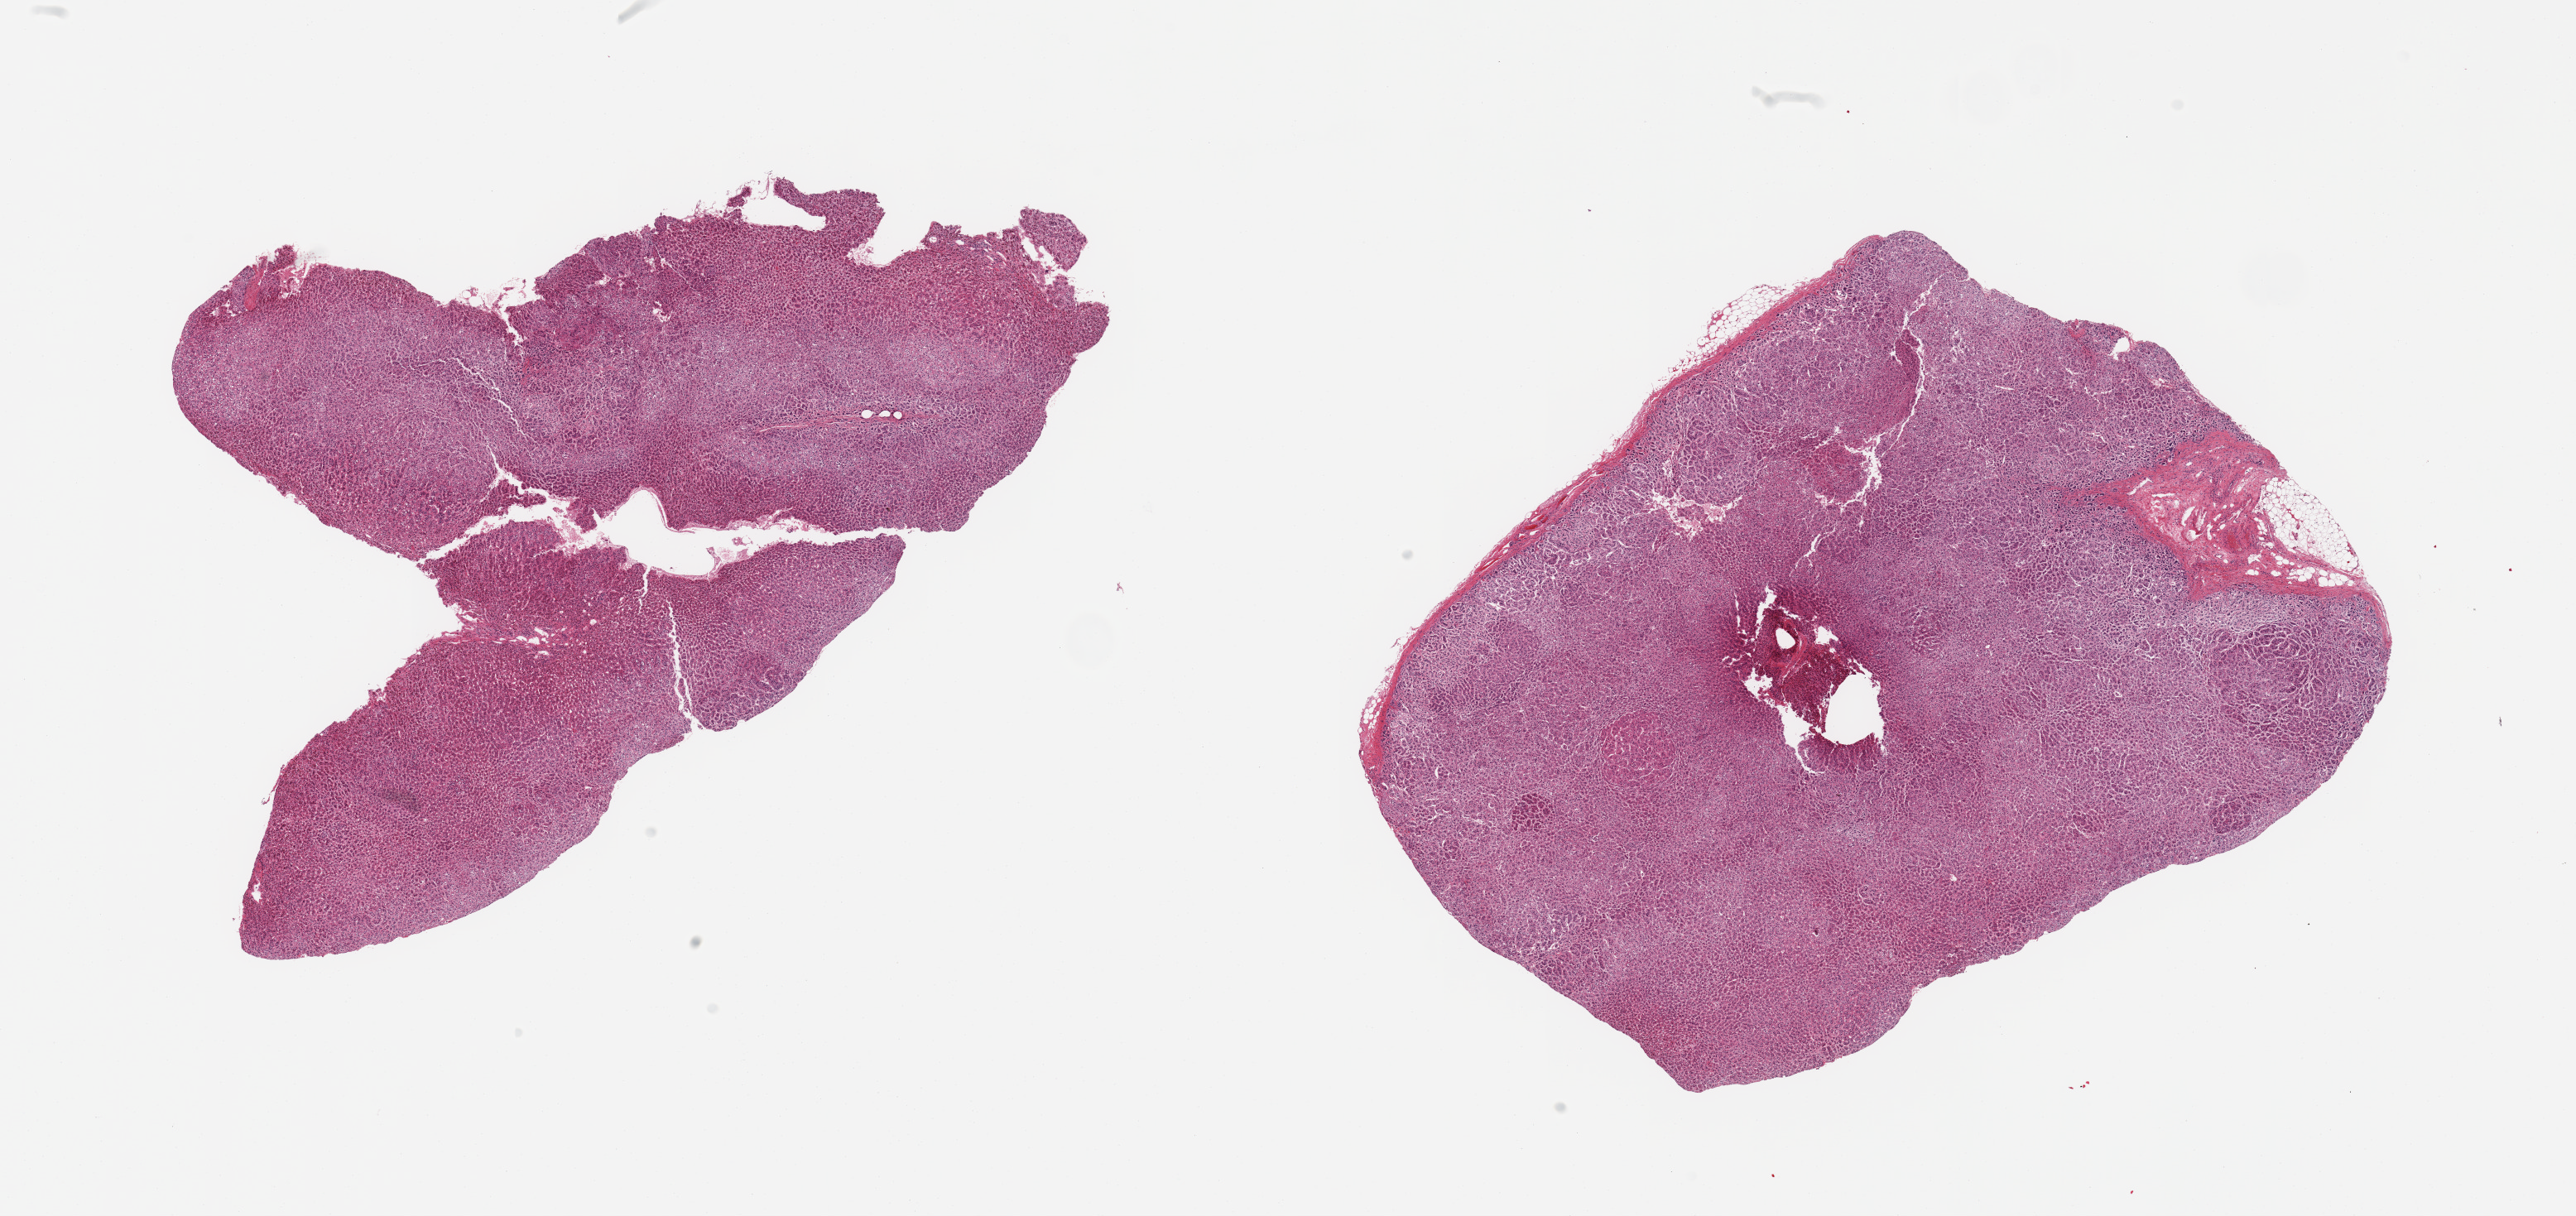
Digitized H&E-stained section — a low-resolution overview of the entire scanned area, about 24.6 x 11.6 mm, PAXgene-fixed, paraffin-embedded tissue, section of adrenal gland (target tissue), tissue donor sample. Donor: male.
Pathologist's review note for this sample: 2 pieces, all cortex, trace adherent fat.